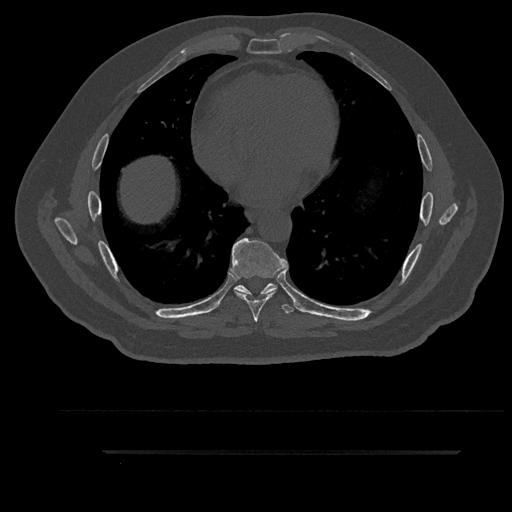
CT including the spine, one axial slice. Slice 507 of 797 in the series (ordered by position). 120 kVp. Bone window (W 1800 / L 400 HU). 0.5 mm slice thickness. 512 × 512 image matrix, field of view 432 × 432 mm. Male patient, age 63 years. Case-level facts recorded for this patient, not image findings: primary cancer: renal; vertebrae with lytic lesions (as recorded): T8.
Annotated regions visible in this slice (semi-automatic segmentation, software-assisted and operator-edited):
- T6 vertebra: box from (x=242, y=292) to (x=269, y=296) px
- T7 vertebra: (x=230, y=238)–(x=289, y=322)
- T8 vertebra: (x=215, y=283)–(x=297, y=314)